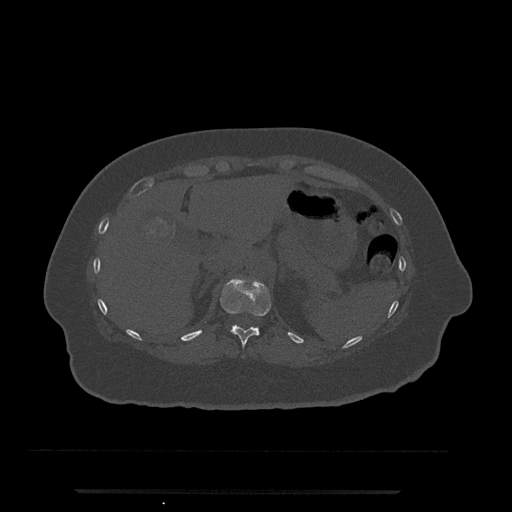
CT including the spine, one axial slice; slice 219 of 797 in the series (ordered by position); reconstruction kernel Br40s/3; bone window (W 1800 / L 400 HU); 512 × 512 image matrix, field of view 440 × 440 mm. Female patient, age 51 years. From the clinical record (not read from this slice): primary cancer: neuro; vertebrae with lytic lesions (as recorded): T8.
Annotated regions visible in this slice (semi-automatic segmentation, software-assisted and operator-edited):
- T11 vertebra: box from (x=220, y=277) to (x=271, y=348) px